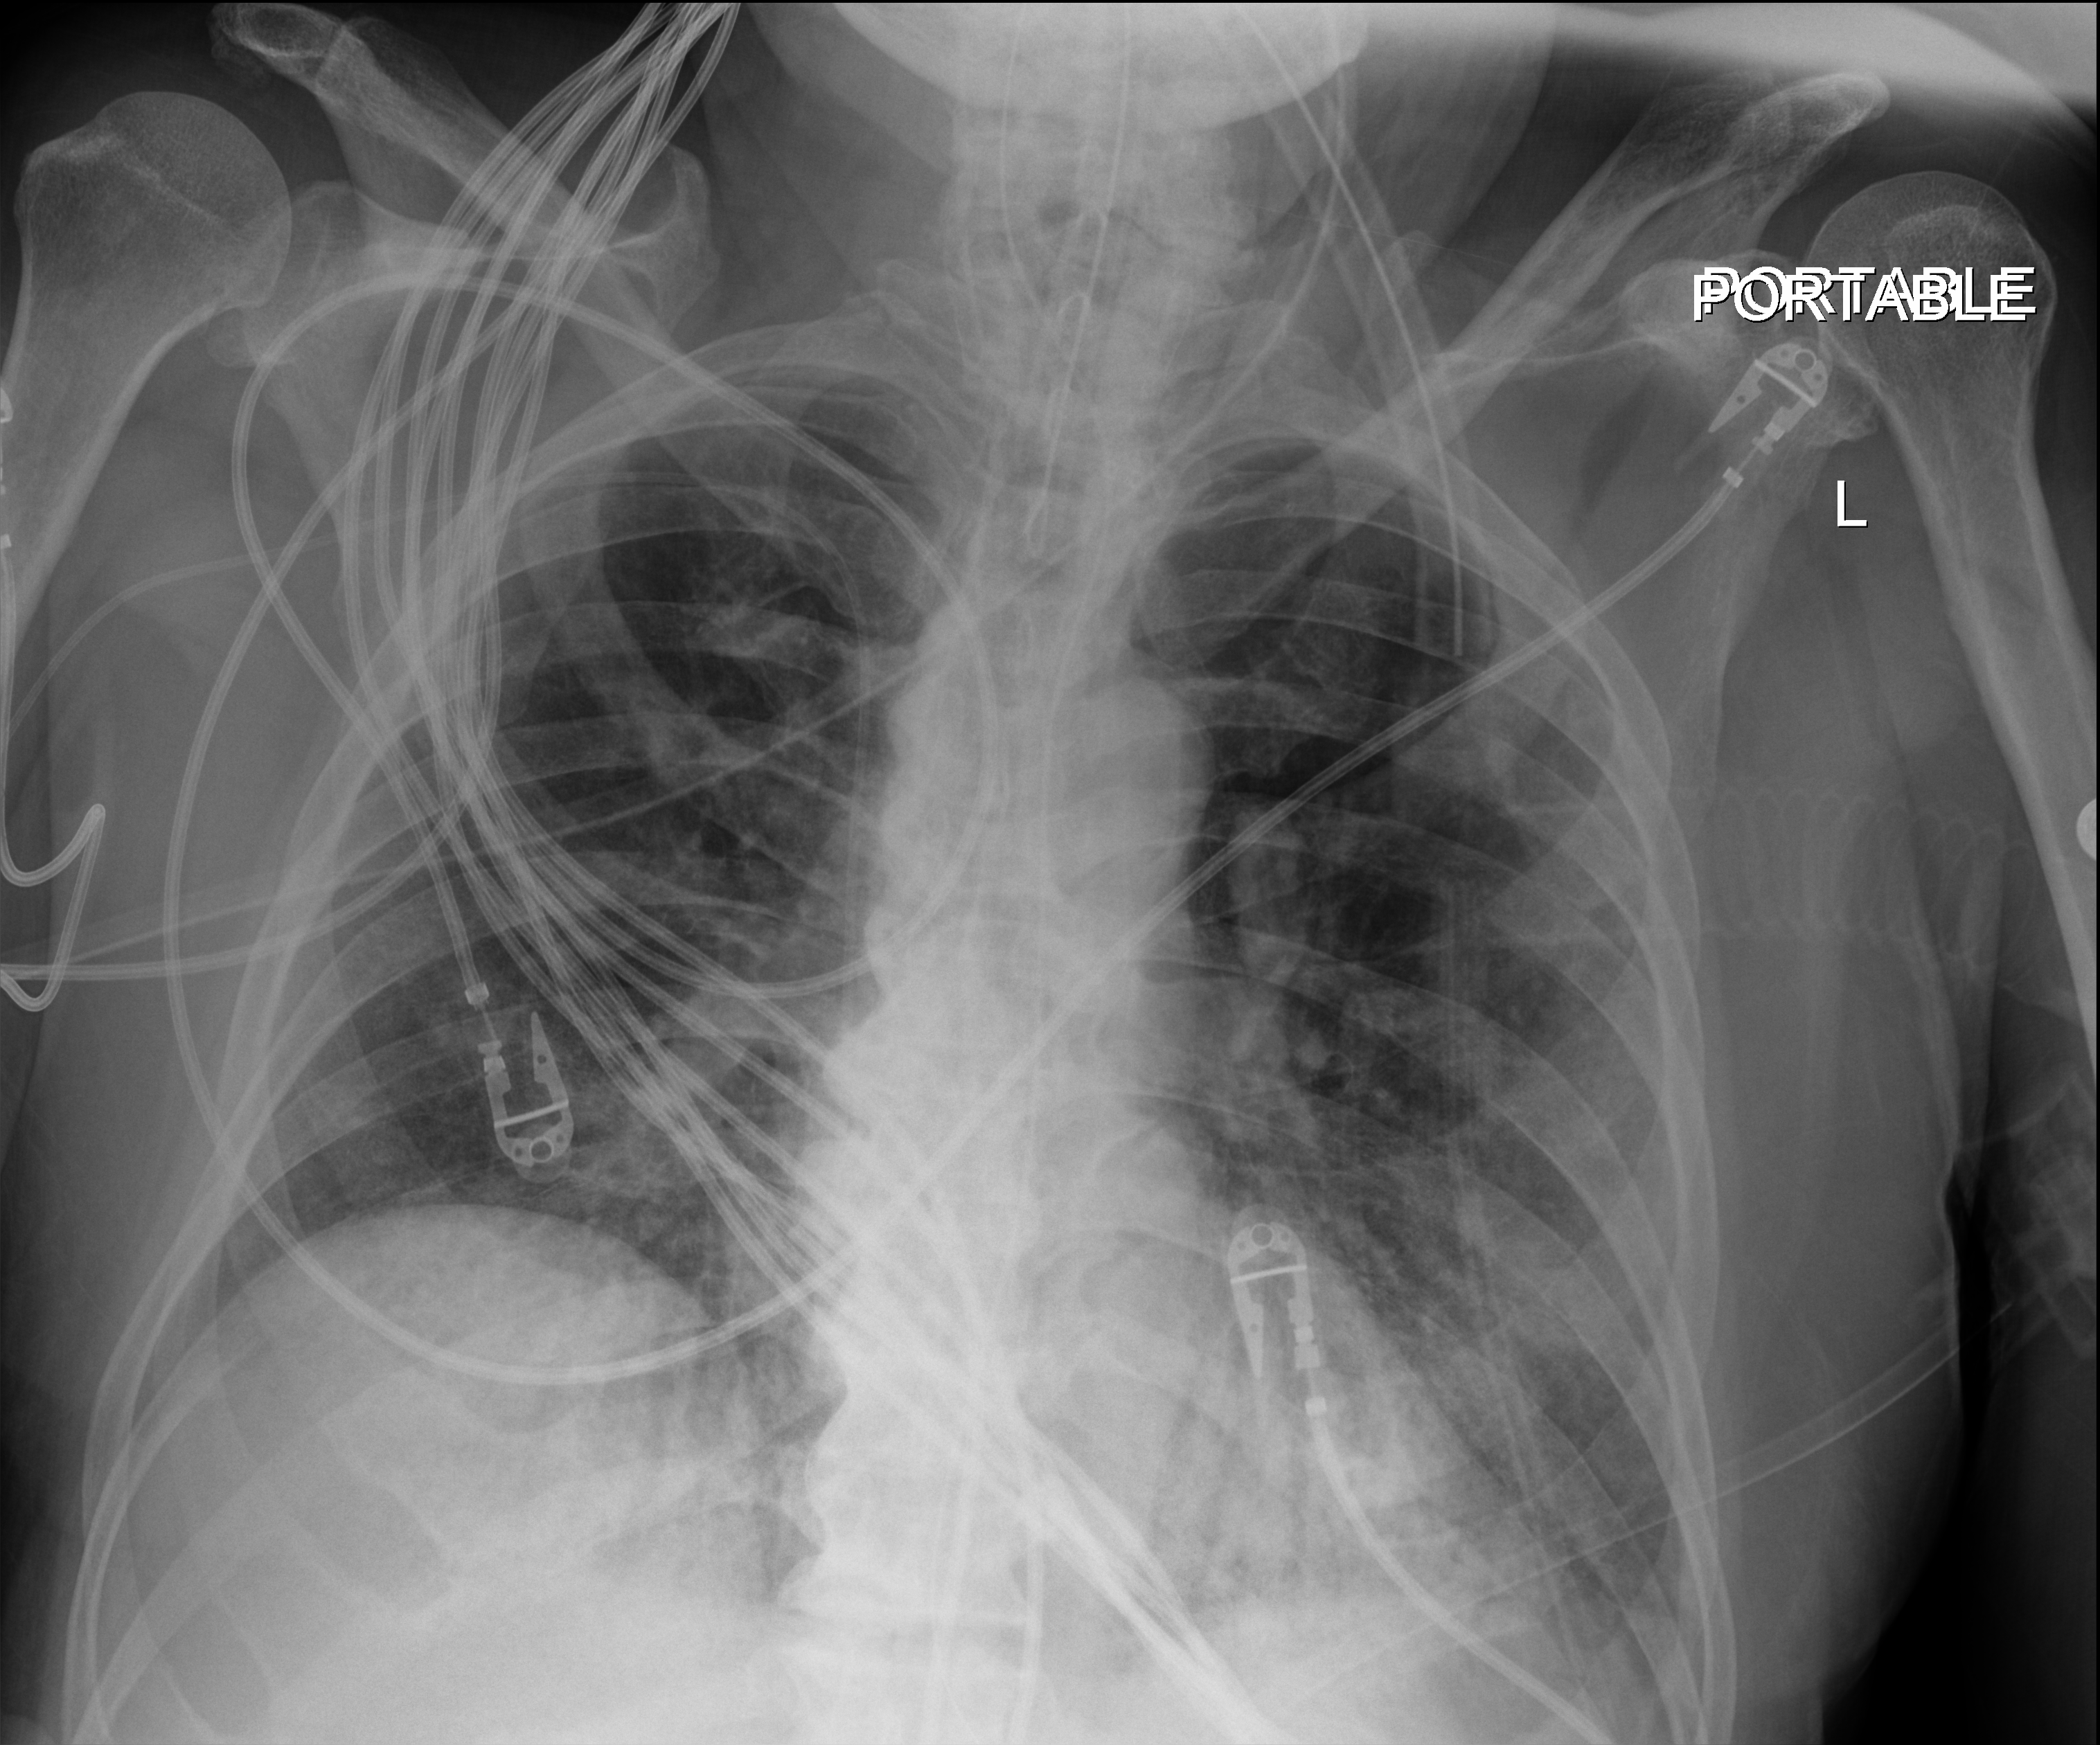
Chest X-ray (portable). Patient hospitalised with COVID-19; male, aged 75–90 years.
Hospital-stay facts (about this admission, not read from this image; timing relative to this image not recorded):
- diabetes (admission record): no